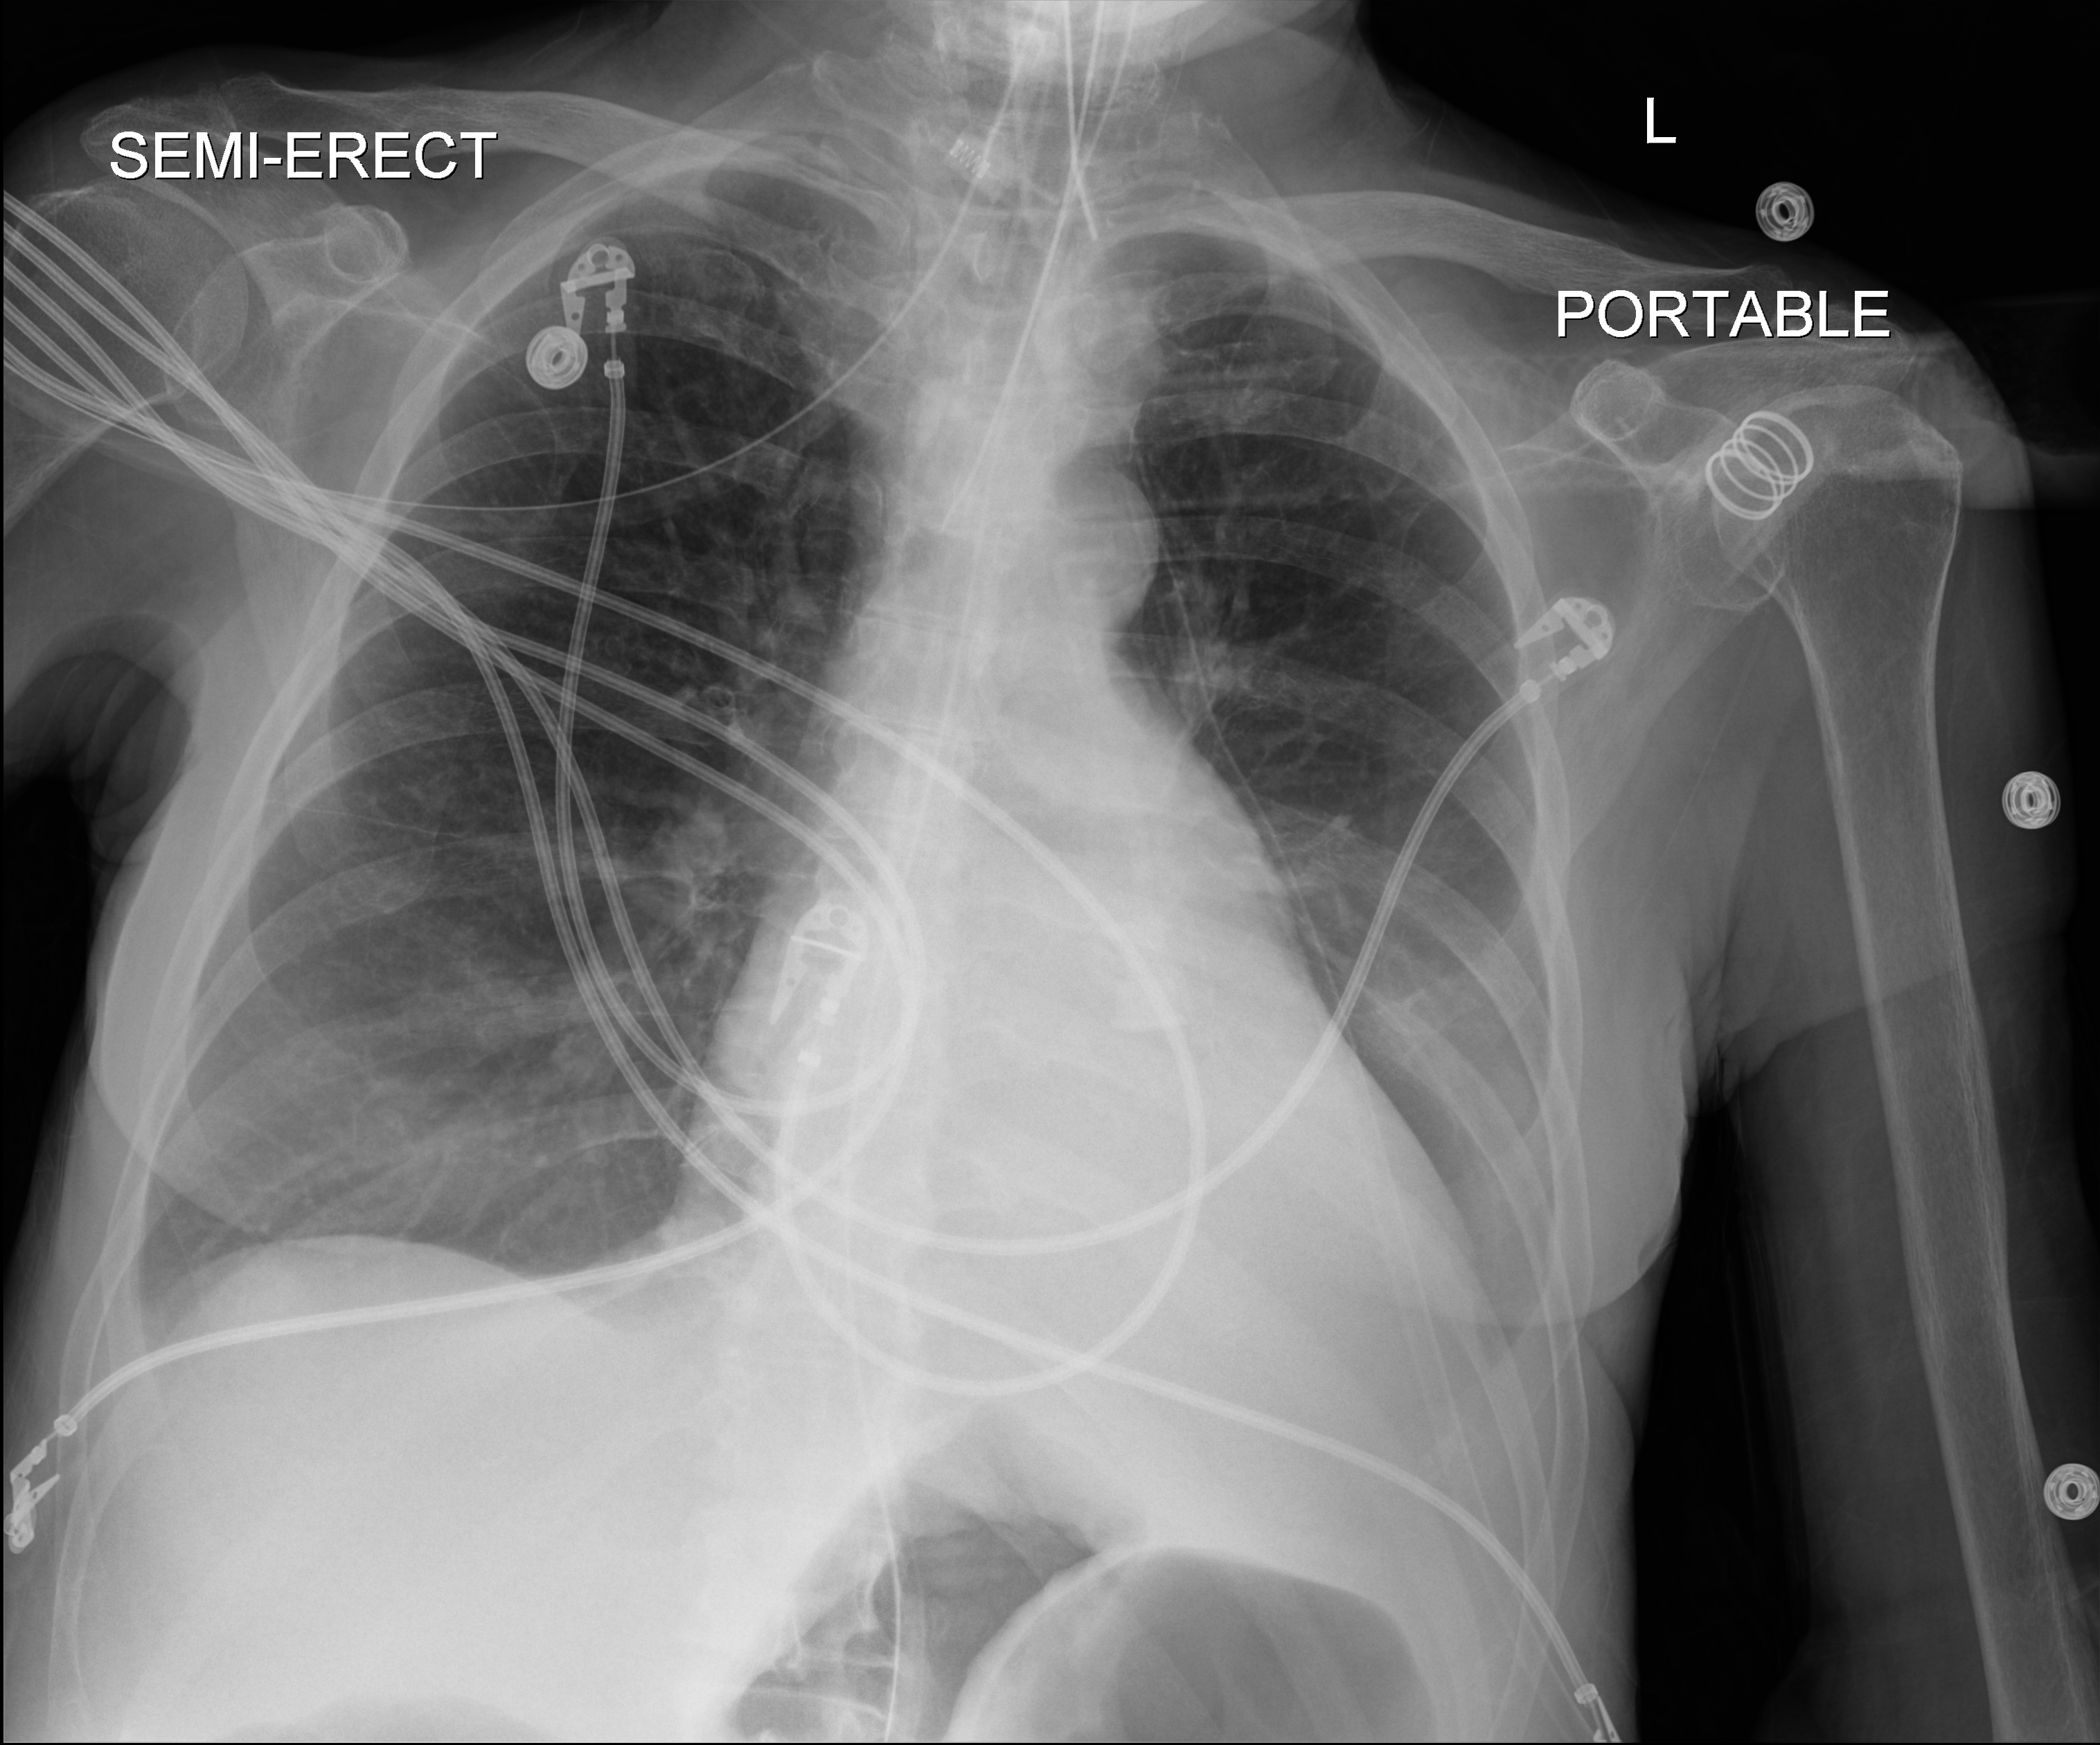
Bedside chest radiograph (digital radiography). Patient hospitalised with COVID-19; female, aged 60–74 years.
Admission-level facts for this patient (not findings on this image; timing relative to this image not recorded):
- mechanically ventilated during this hospital stay: yes
- admitted to intensive care during this hospital stay: yes